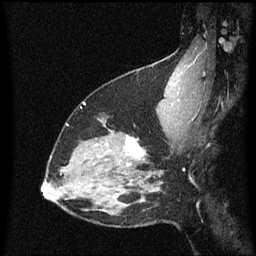
Breast MRI (dynamic contrast-enhanced), one sagittal slice. Slice 45 of 60 in the series (ordered by position). Dynamic contrast-enhanced series, image 2 of 3 at this slice position (ordered by acquisition). 1.5 T. TE 4.2 ms, TR 8.4 ms. 2 mm slice thickness. 256 × 256 image matrix, field of view 200 × 200 mm. Female patient, age 38 years. From the clinical record (not read from this slice): setting: breast cancer imaged before/during neoadjuvant chemotherapy; receptor status: HR-positive, HER2-negative.
Structures marked on this image (semi-automatically segmented with operator editing):
- analysis volume of interest (the breast-tissue region the enhancement analysis was run in; not a lesion): bounding box <122,132,149,163> (left, top, right, bottom; pixels)
- tumour enhancement mask (voxels above the 70 % enhancement threshold inside the analysis volume of interest): <126,136,146,159>